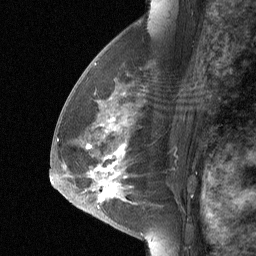
Breast MRI (dynamic contrast-enhanced), one sagittal slice. Position 37 of 64 along the scan axis. Dynamic contrast-enhanced study with each time point stored as its own series, time point 2 of 3 at this slice position (early post-contrast, ordered by acquisition time). 1.5 T. TE 4.8 ms, TR 27 ms. 2 mm slice thickness. 256 × 256 image matrix. Female patient, age 56 years. From the clinical record (not read from this slice): setting: breast cancer imaged before/during neoadjuvant chemotherapy; receptor status: HER2-positive.
Structures marked on this image (semi-automatically segmented with operator editing):
- analysis volume of interest (the breast-tissue region the enhancement analysis was run in; not a lesion): box from (x=68, y=83) to (x=147, y=214) px
- tumour enhancement mask (voxels above the 90 % enhancement threshold inside the analysis volume of interest): (x=96, y=119)–(x=125, y=202)